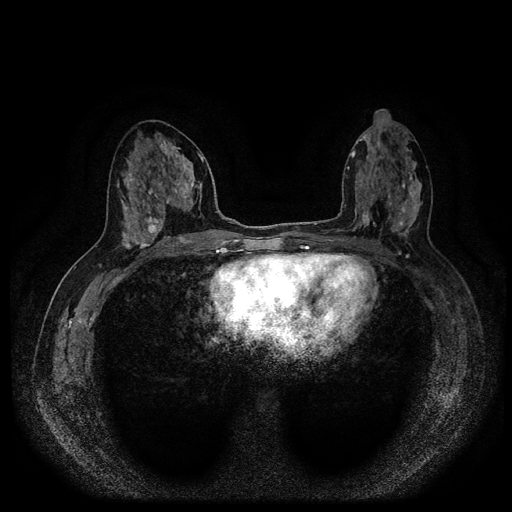
Breast MRI (dynamic contrast-enhanced, multi-phase), one axial slice. Position 47 of 116 along the scan axis. Dynamic contrast-enhanced series, time point 2 of 5 at this slice position (early post-contrast). 1.5 T. TE 2.6 ms, TR 5.4 ms. 512 × 512 image matrix. Patient: female, 48 years.
Annotated regions visible in this slice (semi-automatic segmentation, software-assisted and operator-edited):
- breast lesion (labelled 'tumour' in the annotation; benign lesions carry a separate 'benign' label): box from (x=146, y=211) to (x=160, y=237) px